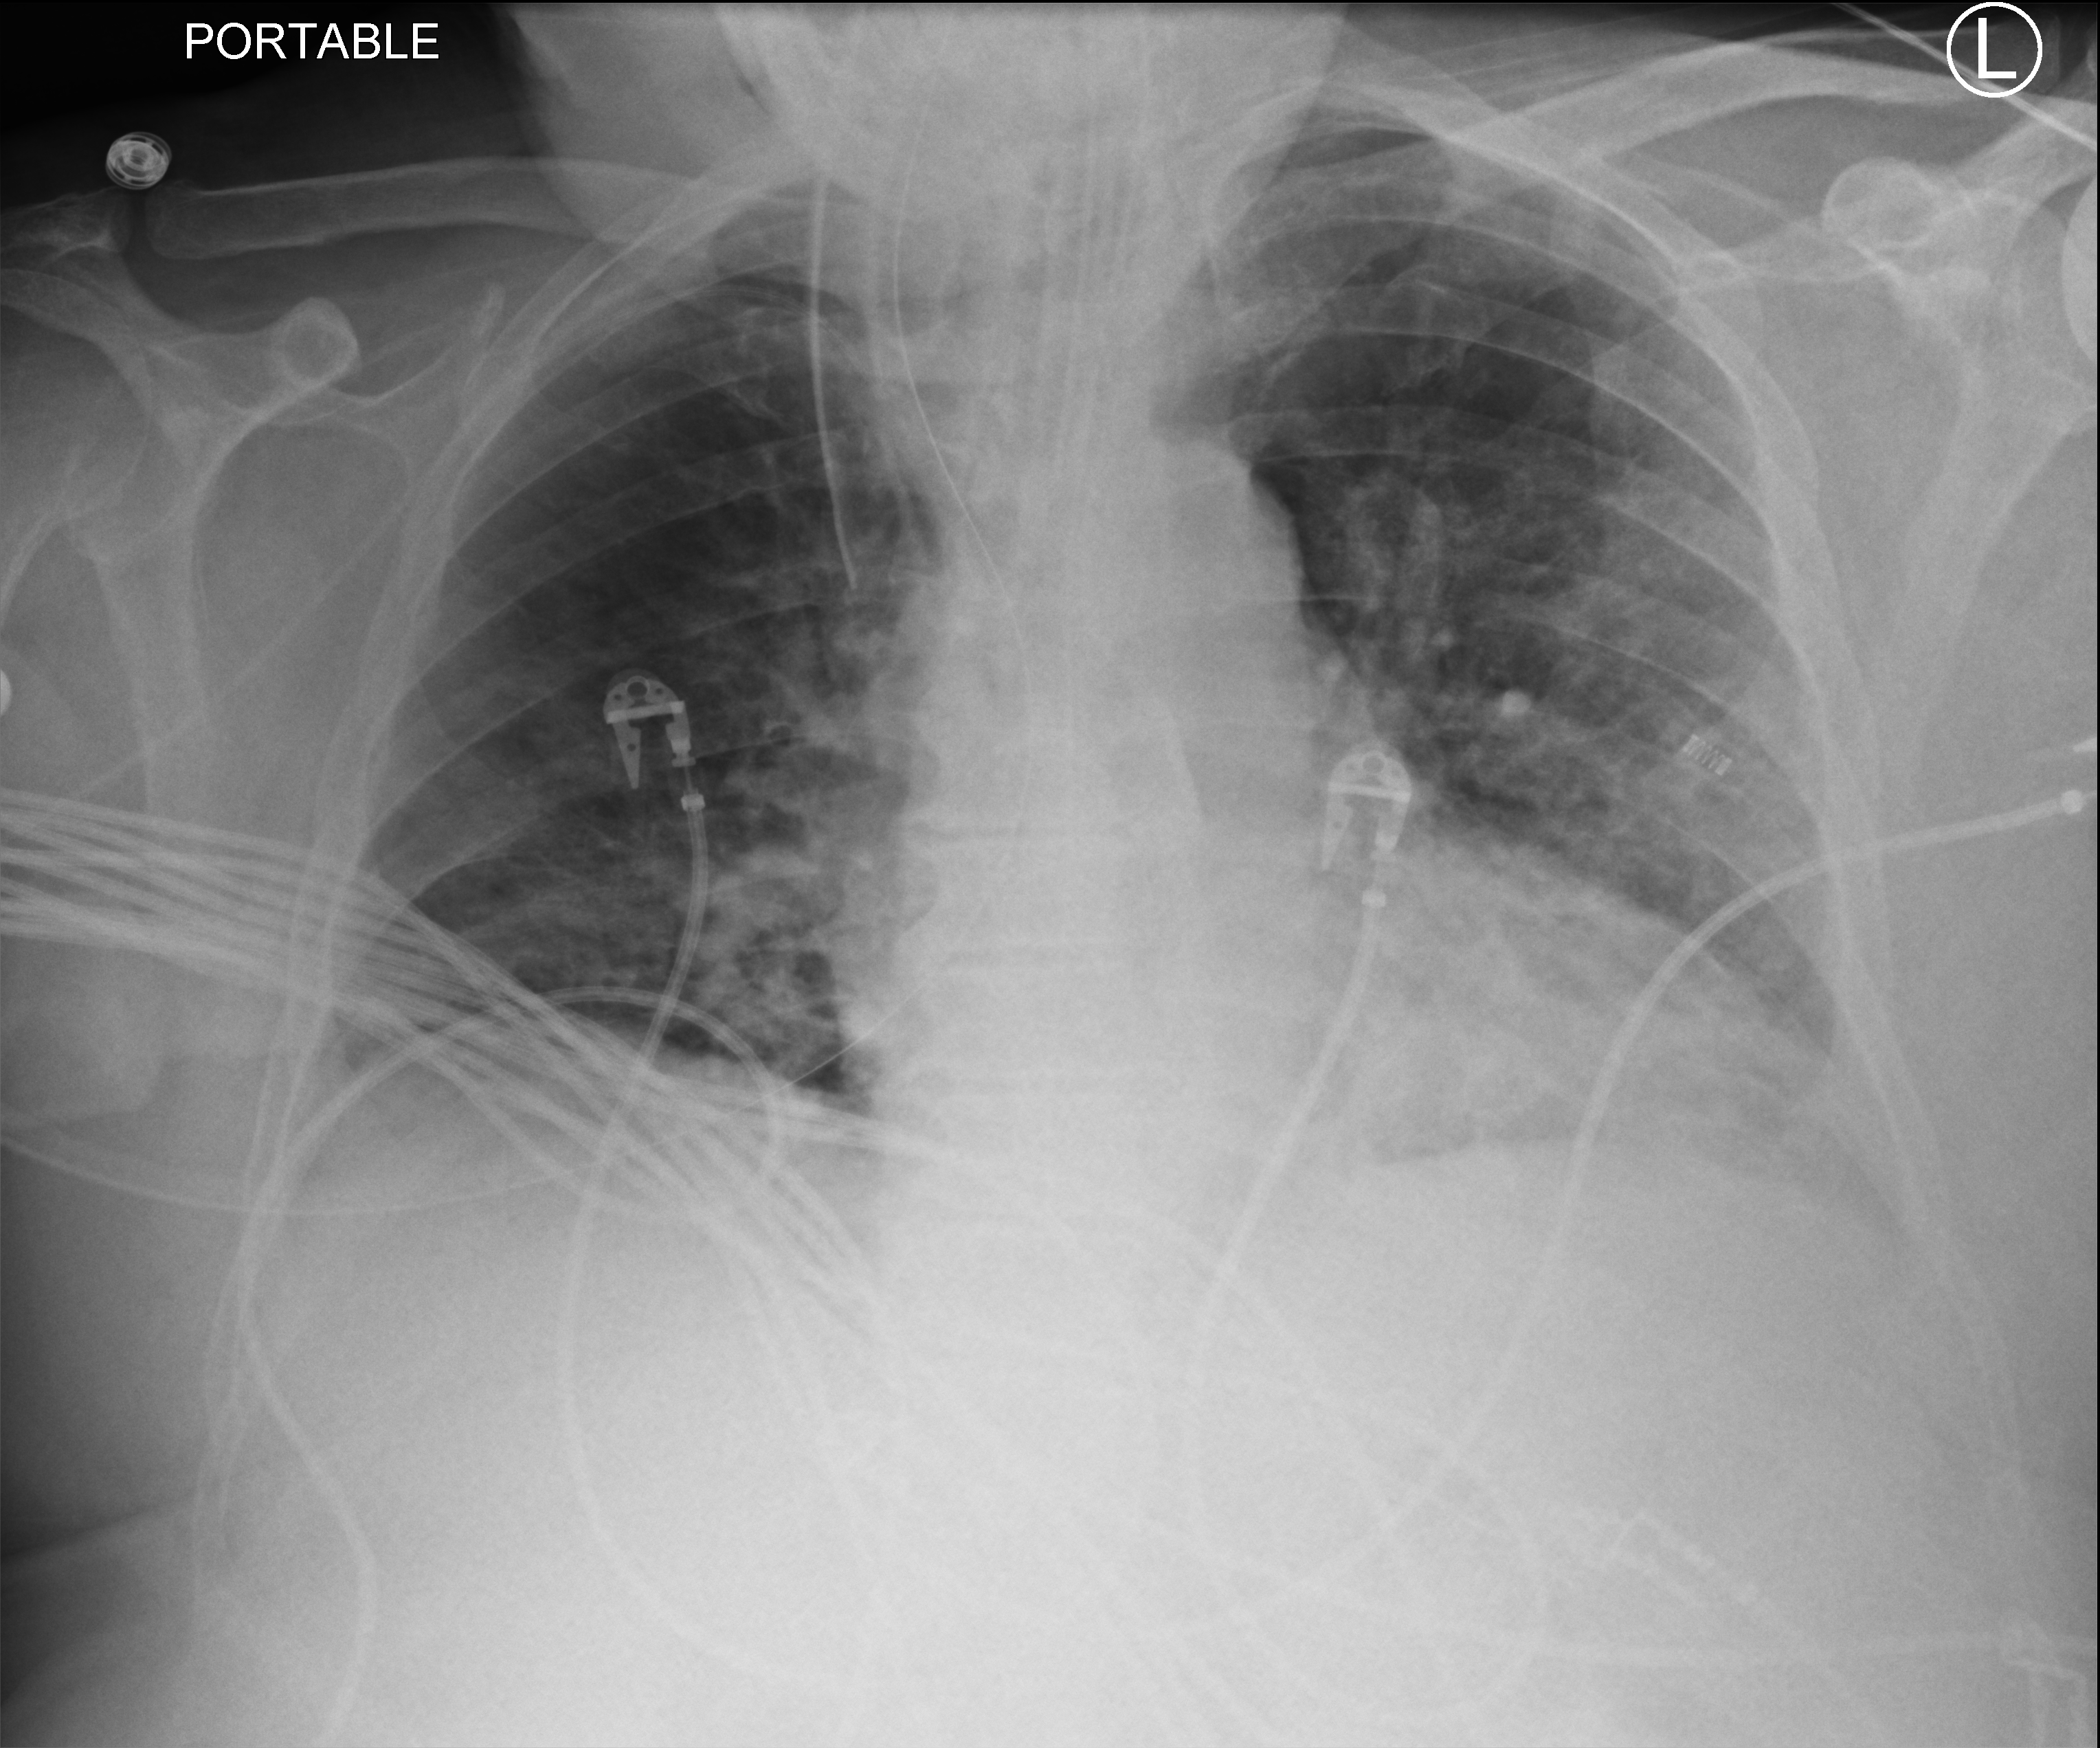
Portable chest radiograph; anteroposterior (AP) projection. Male patient hospitalised with COVID-19, age 60–74 years.
Hospital-stay facts (about this admission, not read from this image; timing relative to this image not recorded): admitted to intensive care during this hospital stay: yes; diabetes (admission record): no; mechanically ventilated during this hospital stay: yes.